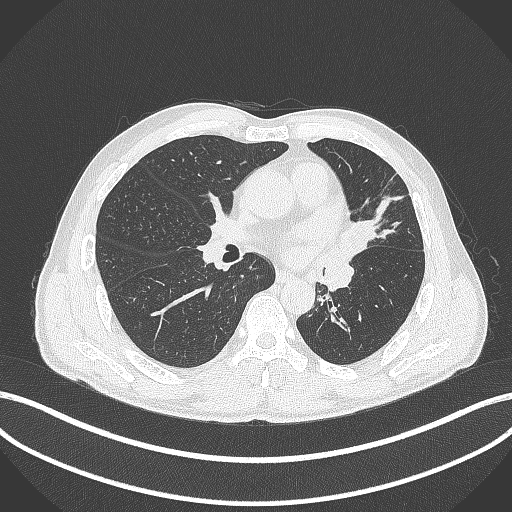
Chest CT, one axial slice. Slice 224 of 429 in the series (ordered by position). Reconstruction kernel B70f. Lung window (W 1500 / L -600 HU). 512 × 512 image matrix, field of view 400 × 400 mm. Patient: male, 57 years. Case-level facts recorded for this patient, not image findings: clinical TNM (as recorded): T2b N0 M0.
Structures marked on this image (rectangle marked by the reading radiologist):
- lung tumour (recorded histology: squamous cell carcinoma): bounding box <340,213,381,259> (left, top, right, bottom; pixels)